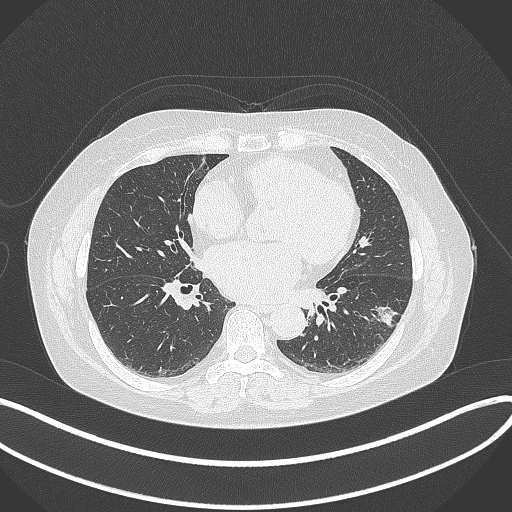
Chest CT, one axial slice. Slice 160 of 373 in the series (ordered by position). Reconstruction kernel B70f. Lung window (W 1500 / L -600 HU). 1 mm slice thickness. 512 × 512 image matrix, field of view 400 × 400 mm. Female patient, age 67 years. Case-level facts recorded for this patient, not image findings: clinical TNM (as recorded): T1c N0 M0; histopathological grade: G2.
Structures marked on this image (rectangle marked by the reading radiologist):
- lung tumour (recorded histology: adenocarcinoma): bounding box [x1, y1, x2, y2] px = [366, 300, 400, 332]